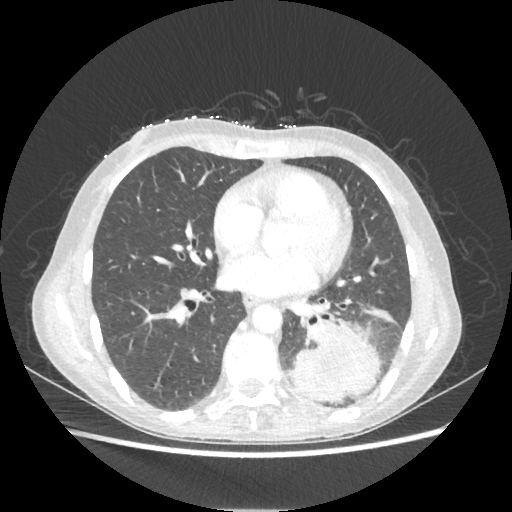
Chest CT, one axial slice; slice 97 of 221 in the series (ordered by position); reconstruction kernel STANDARD; 80 kVp; lung window (W 1500 / L -600 HU); 512 × 512 image matrix, field of view 360 × 360 mm. Patient: female, 53 years. Case-level facts recorded for this patient, not image findings: clinical TNM (as recorded): T3 N0 M0.
Annotated regions visible in this slice (rectangle marked by the reading radiologist):
- lung tumour (recorded histology: adenocarcinoma): bounding box <290,321,380,402> (left, top, right, bottom; pixels)